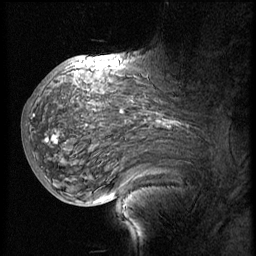
Breast MRI (dynamic contrast-enhanced), one sagittal slice. Position 36 of 60 along the scan axis. 3 images stored at this slice position (order not interpretable as contrast timing). 1.5 T. TE 4.2 ms, TR 8.9 ms. 2.5 mm slice thickness. 256 × 256 image matrix. Patient: female, 57 years. Case-level facts recorded for this patient, not image findings: setting: breast cancer imaged before/during neoadjuvant chemotherapy; receptor status: HER2-positive.
Annotated regions visible in this slice (semi-automatically segmented with operator editing):
- analysis volume of interest (the breast-tissue region the enhancement analysis was run in; not a lesion): bounding box [x1, y1, x2, y2] px = [34, 75, 214, 171]
- tumour enhancement mask (voxels above the 140 % enhancement threshold inside the analysis volume of interest): [47, 120, 173, 141]